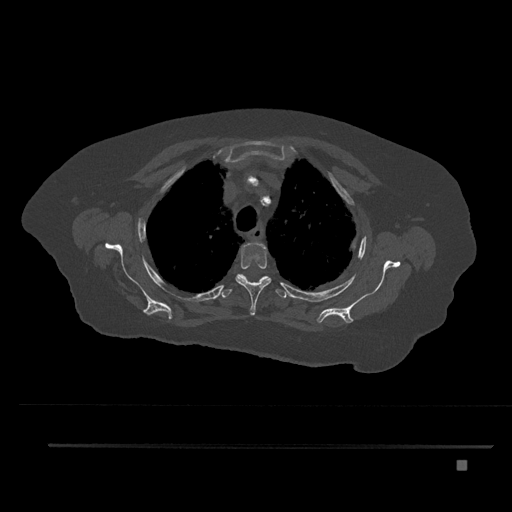
CT including the spine, one axial slice; slice 630 of 797 in the series (ordered by position); reconstruction kernel Br40s/3; 120 kVp; bone window (W 1800 / L 400 HU); 0.5 mm slice thickness; 512 × 512 image matrix, field of view 437 × 437 mm. Female patient, age 76 years. From the clinical record (not read from this slice): primary cancer: lung.
Outlined on this slice (semi-automatic segmentation, software-assisted and operator-edited):
- T3 vertebra: bounding box <235,242,272,316> (left, top, right, bottom; pixels)
- T4 vertebra: <220,274,287,298>